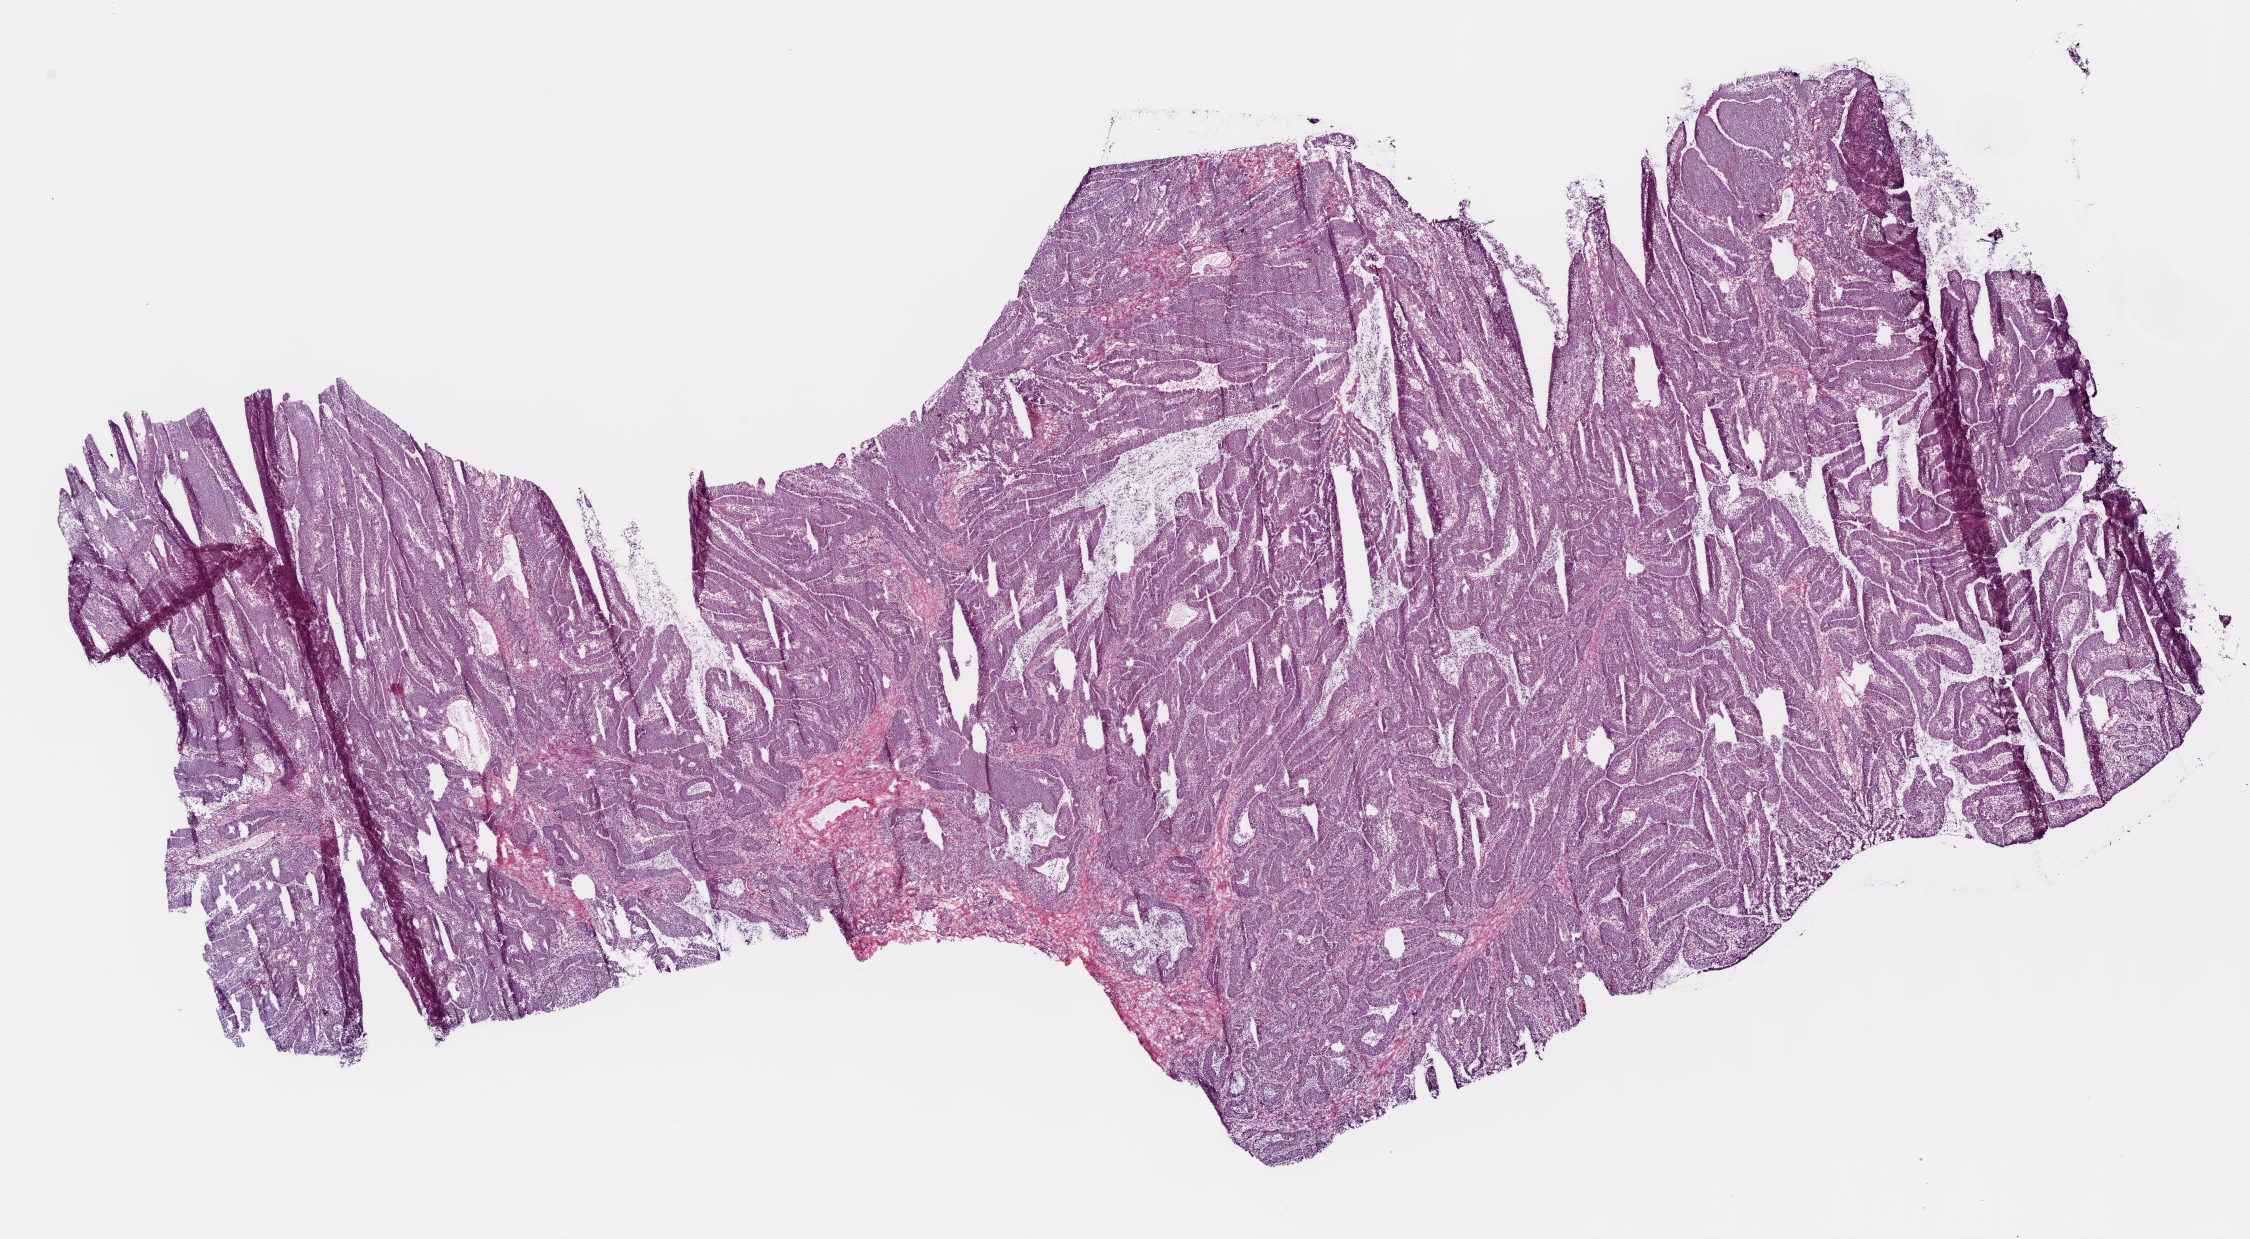
Digitized Hematoxylin and eosin (H&E) stained tissue section (whole slide) — low-resolution overview of the scanned area, about 18.1 x 9.9 mm (slide scanned at 20x). Frozen section from the bottom of the tissue portion. Primary tumour sample from the rectum. Male, age 77 years at initial diagnosis. Pathologist review of this section (percent, as recorded): tumour cells 85%, tumour nuclei 80%, normal cells 0%, stromal cells 15%, necrosis 0%. Inflammatory infiltration, as recorded: lymphocyte infiltration 10%.
AJCC pathologic stage: IIA. Lymph nodes positive (case pathology): 0 of 25 examined. Pathologic diagnosis: Mucinous adenocarcinoma.